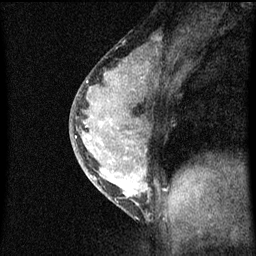
Breast MRI (dynamic contrast-enhanced), one sagittal slice. Position 34 of 60 along the scan axis. Dynamic contrast-enhanced series, image 2 of 3 at this slice position (ordered by acquisition). 1.5 T. TE 4.2 ms, TR 8 ms. 256 × 256 image matrix, field of view 180 × 180 mm. Patient: female, 33 years.
Annotated regions visible in this slice (semi-automatic segmentation, software-assisted and operator-edited):
- analysis volume of interest (the breast-tissue region the enhancement analysis was run in; not a lesion): box from (x=70, y=56) to (x=162, y=215) px
- tumour enhancement mask (voxels above the 70 % enhancement threshold inside the analysis volume of interest): (x=76, y=72)–(x=150, y=205)